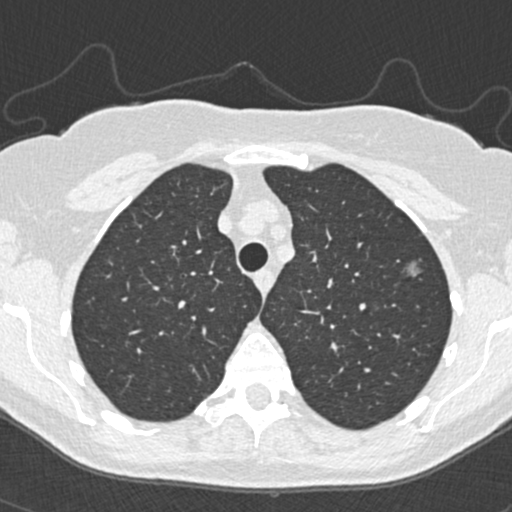
Low-dose screening chest CT, one axial slice; slice 281 of 350 in the series (ordered by position); 120 kVp; lung window (W 1500 / L -600 HU); 1 mm slice thickness; 512 × 512 image matrix, field of view 298 × 298 mm.
Structures marked on this image (outlined manually by an expert reader):
- lesion 3 (tumor, upper lobe of left lung): bounding box [x1, y1, x2, y2] px = [407, 264, 419, 277]